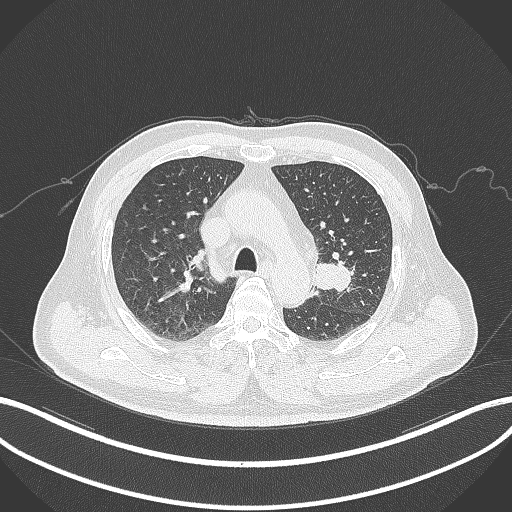
Chest CT, one axial slice; reconstruction kernel B70f; lung window (W 1500 / L -600 HU); 1 mm slice thickness; 512 × 512 image matrix. Male patient, age 67 years. From the clinical record (not read from this slice): clinical TNM (as recorded): T2a N1 M0; histopathological grade: G3.
Annotated regions visible in this slice (bounding box drawn by a radiologist):
- lung tumour (recorded histology: adenocarcinoma): bounding box <311,259,354,293> (left, top, right, bottom; pixels)